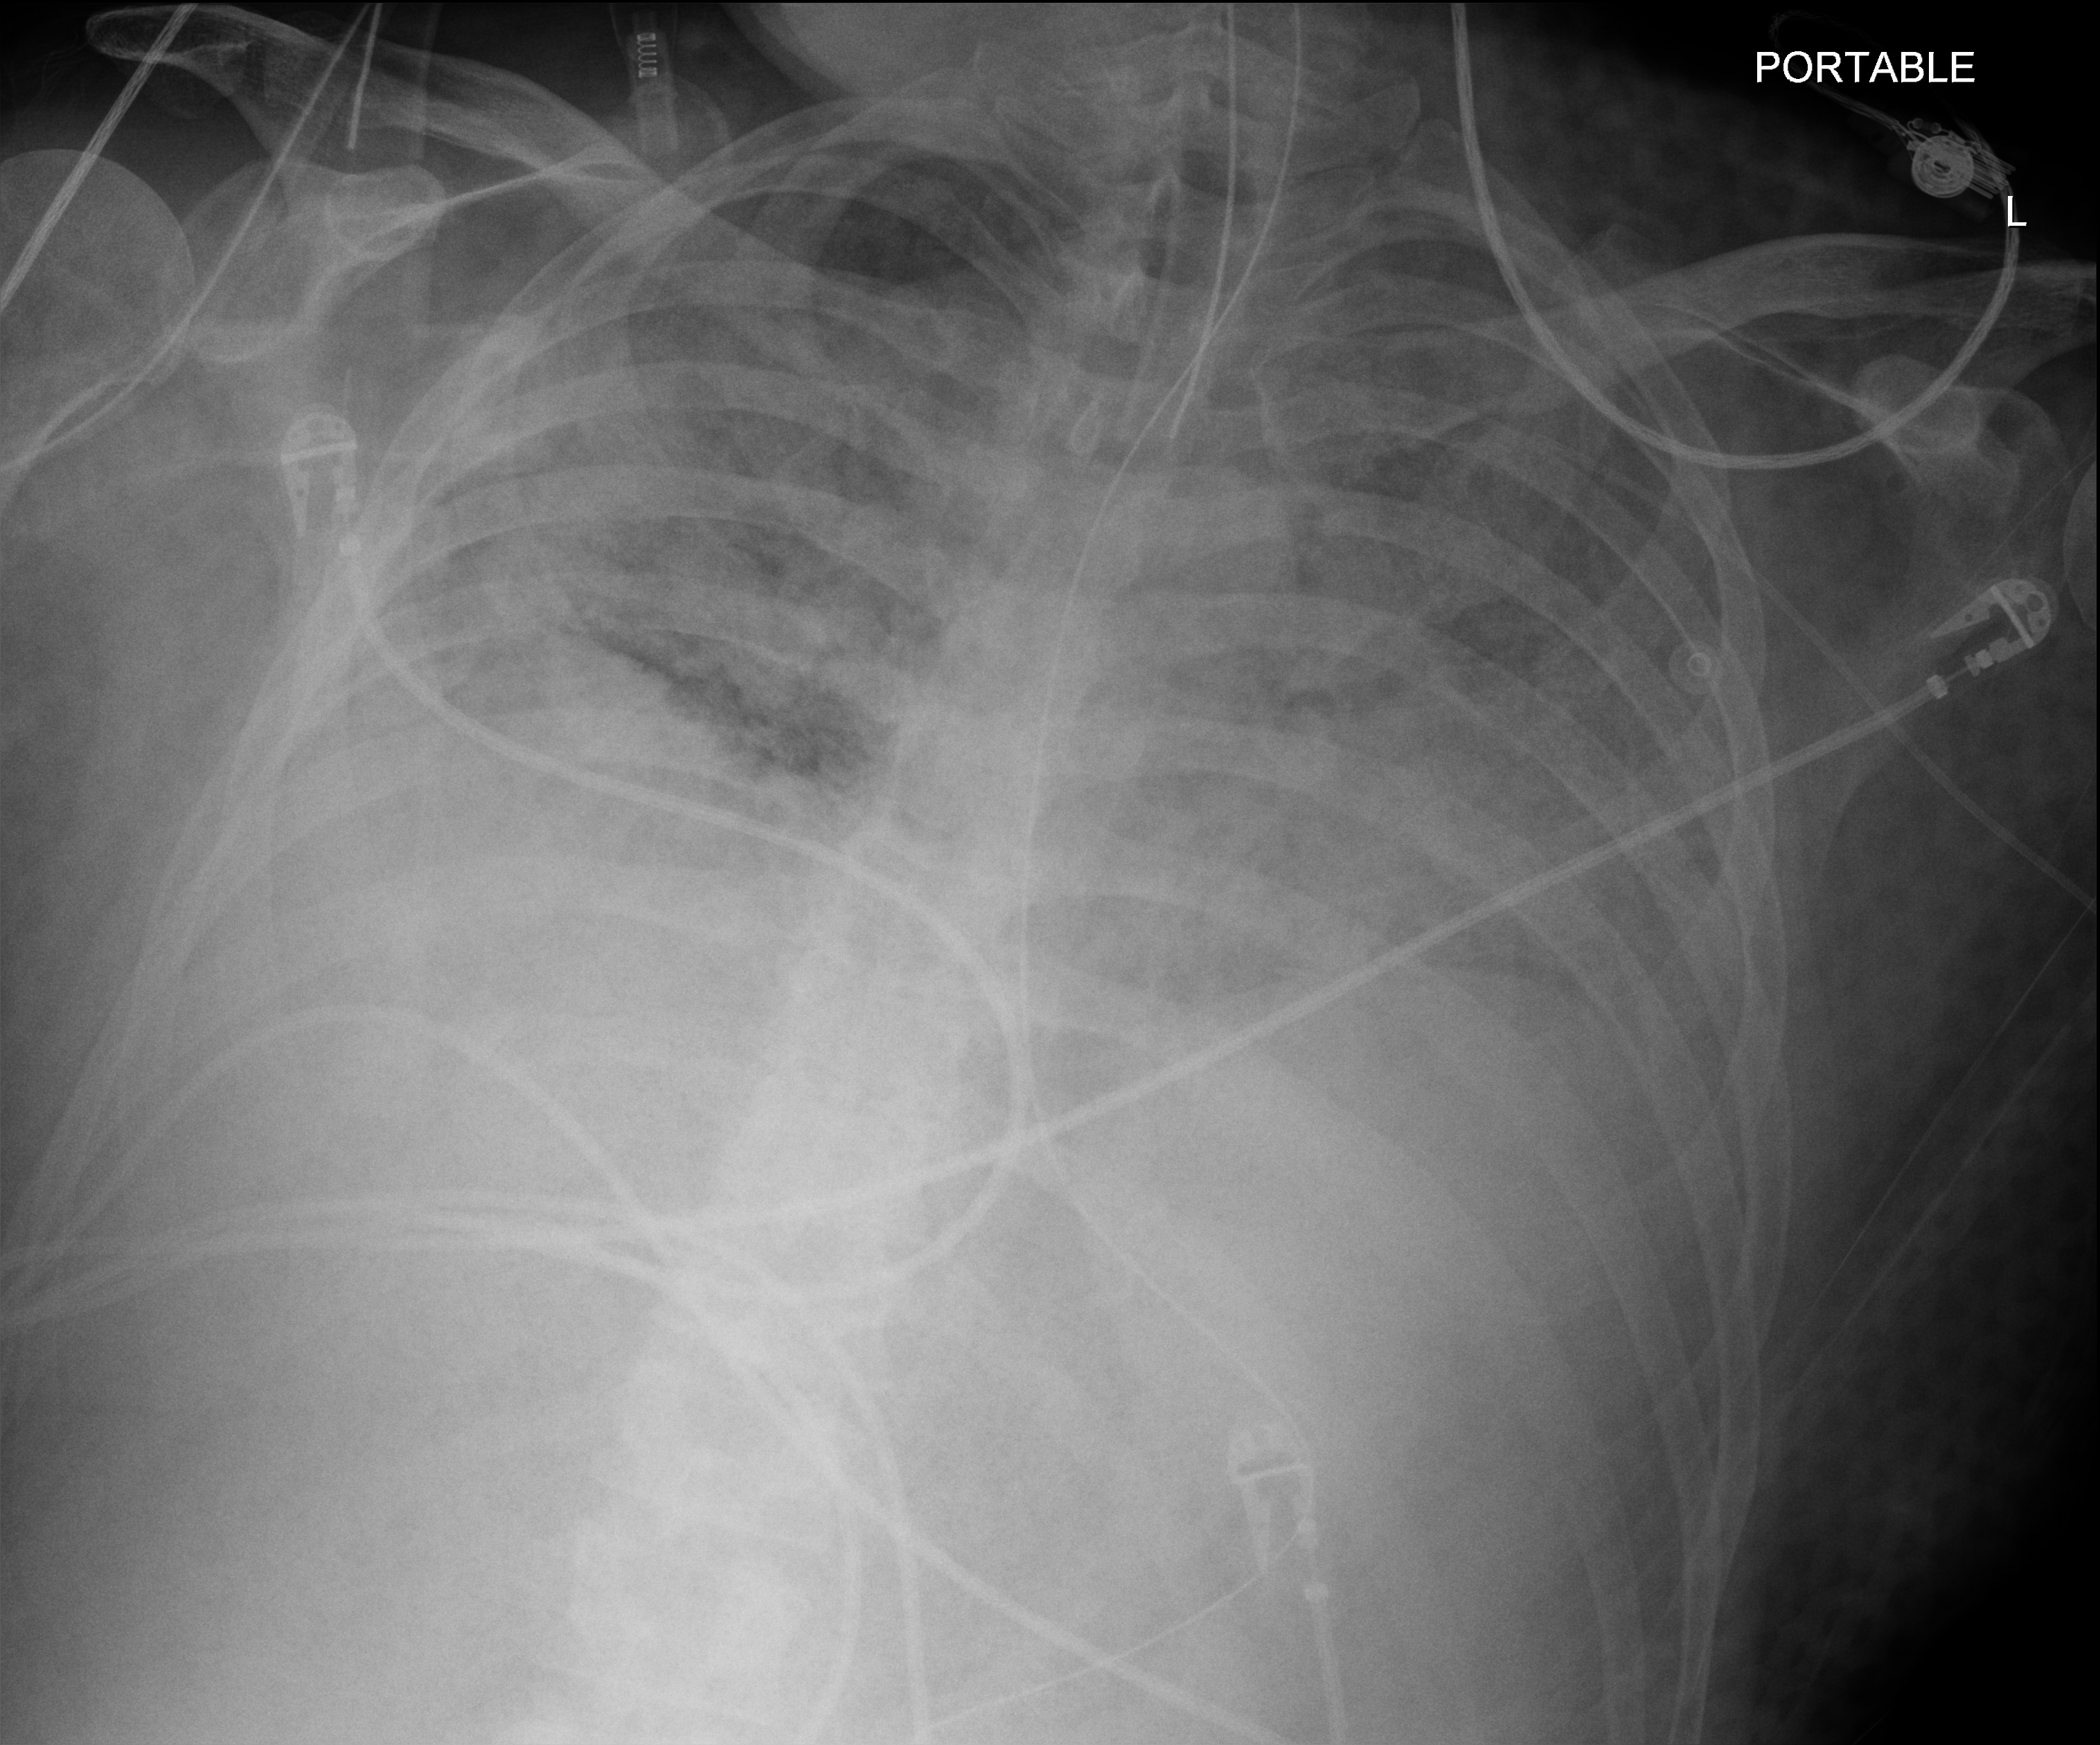
Chest X-ray (portable); anteroposterior (AP) projection. Male patient hospitalised with COVID-19, age 18–59 years.
From the hospital-stay record, not from the radiograph (when in the stay this image was taken is not recorded):
- diabetes (admission record): no
- hypertension (admission record): yes